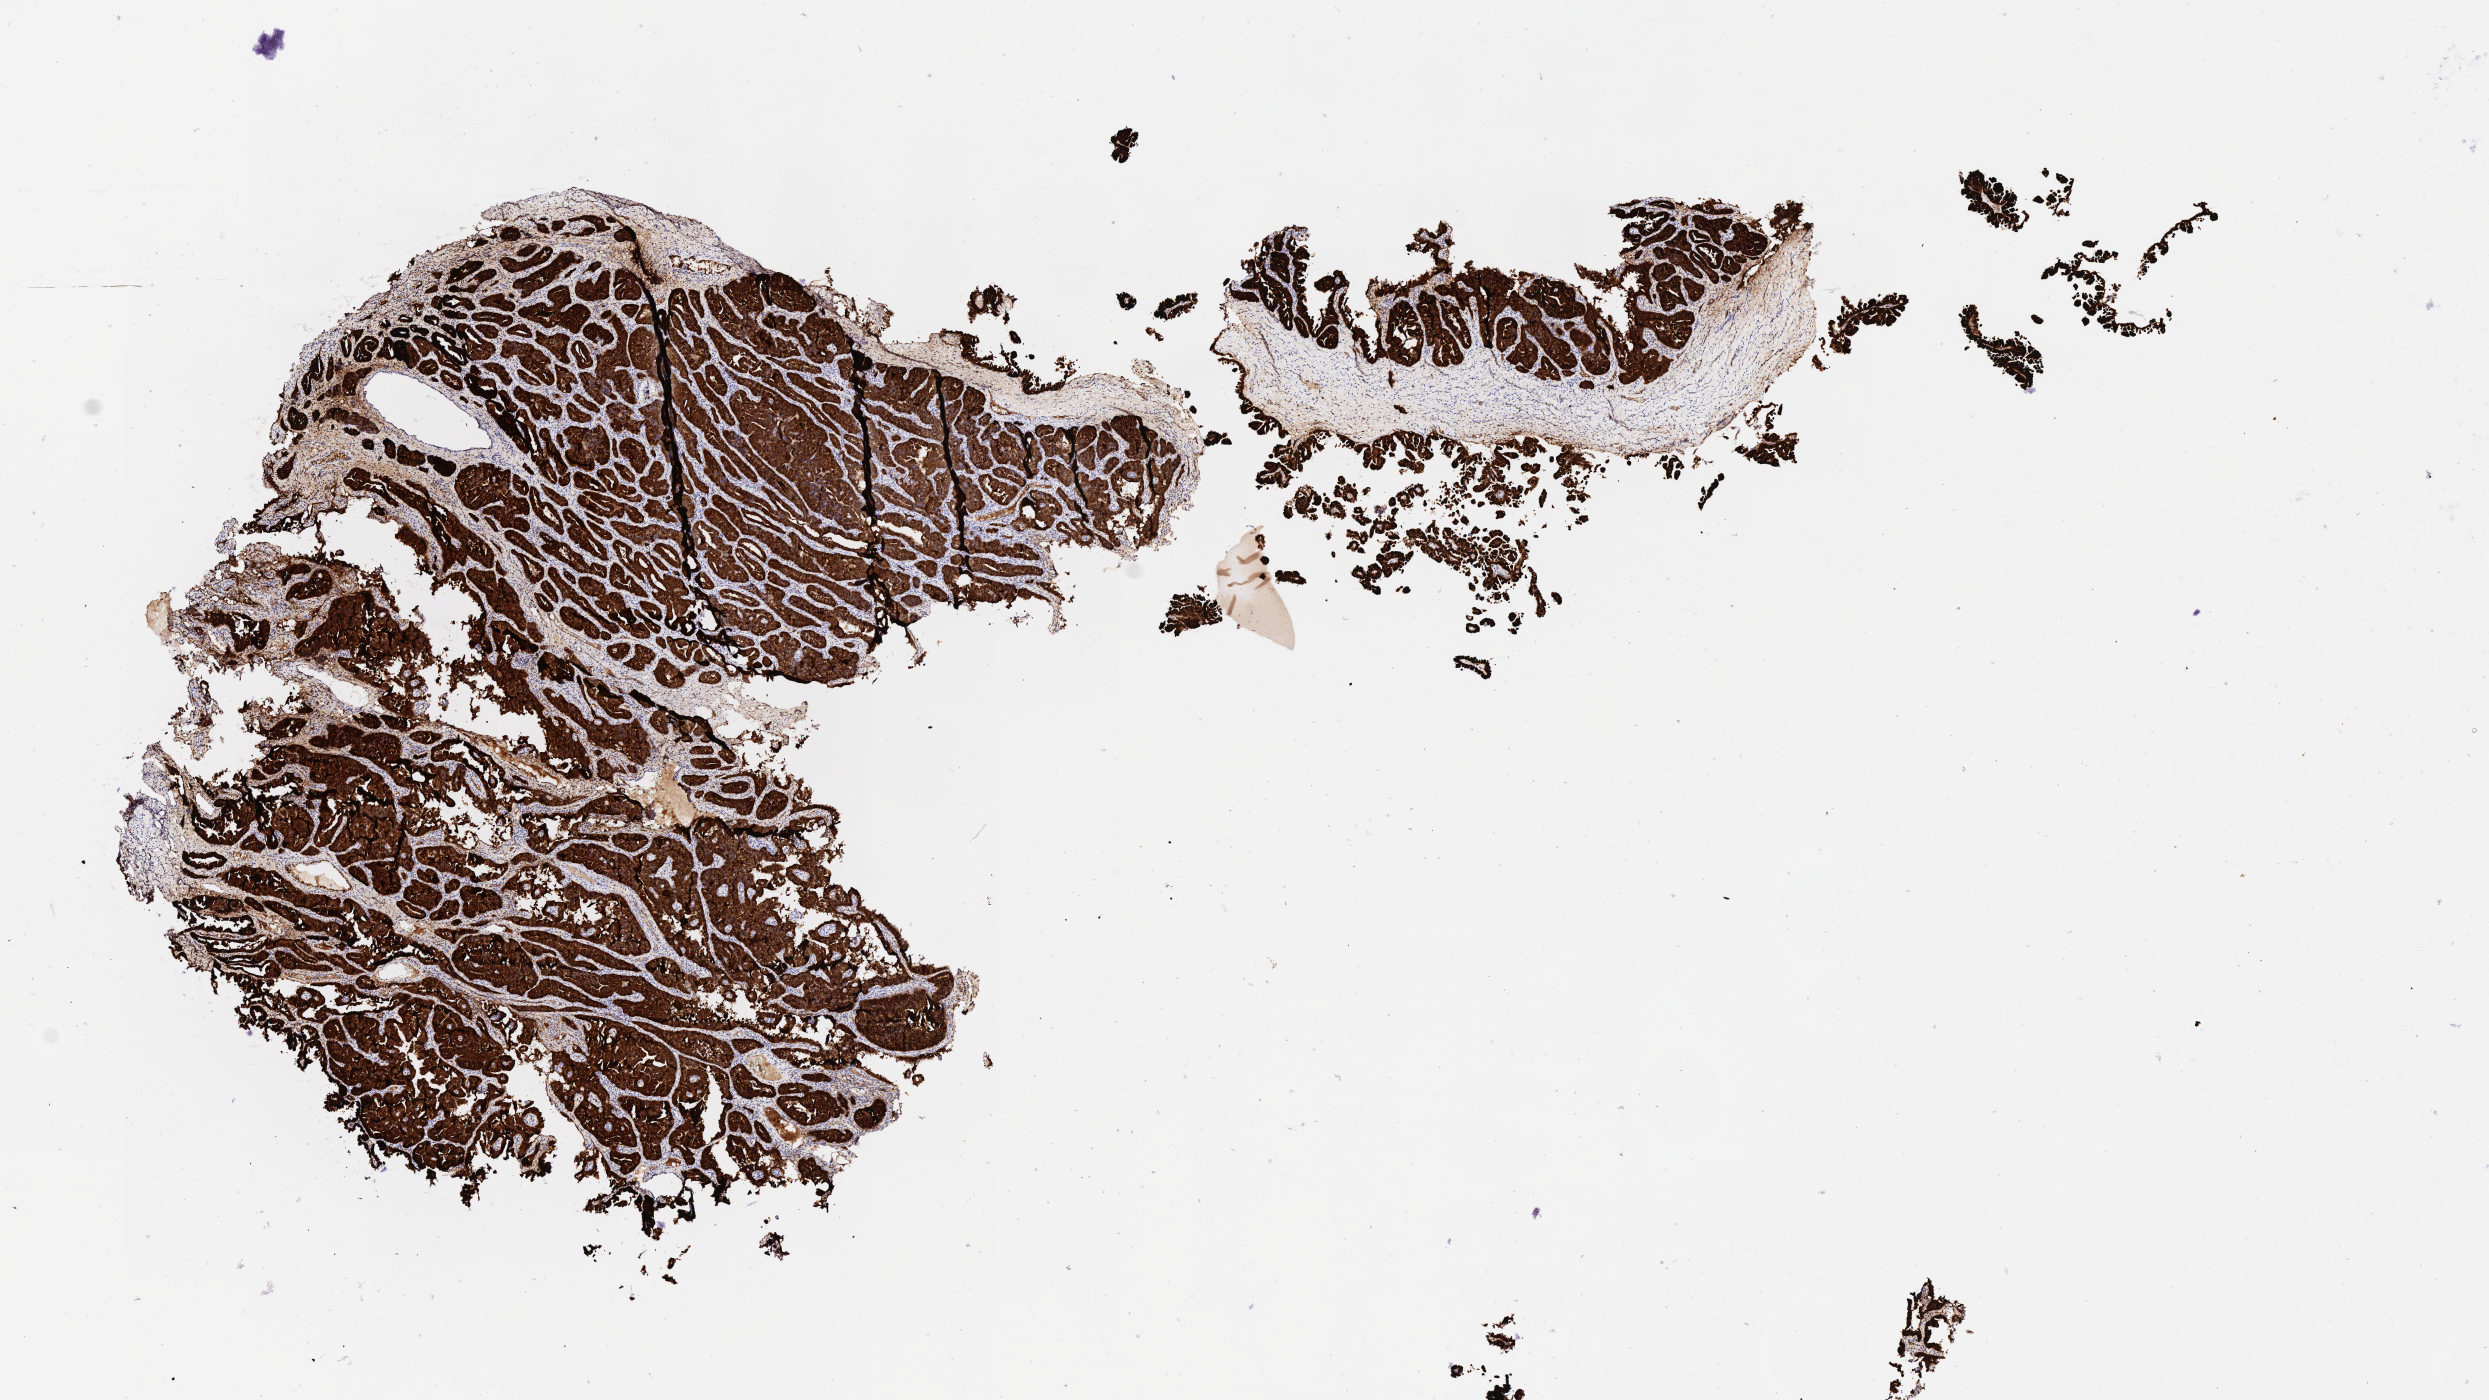
IHC for p16 (p16INK4a), whole-slide image, low-resolution overview of the scanned area, about 10.1 x 5.7 mm; specimen: tumor tissue; site: cervix. Patient female; aged 70.
Diagnosis: Adenocarcinoma, NOS.